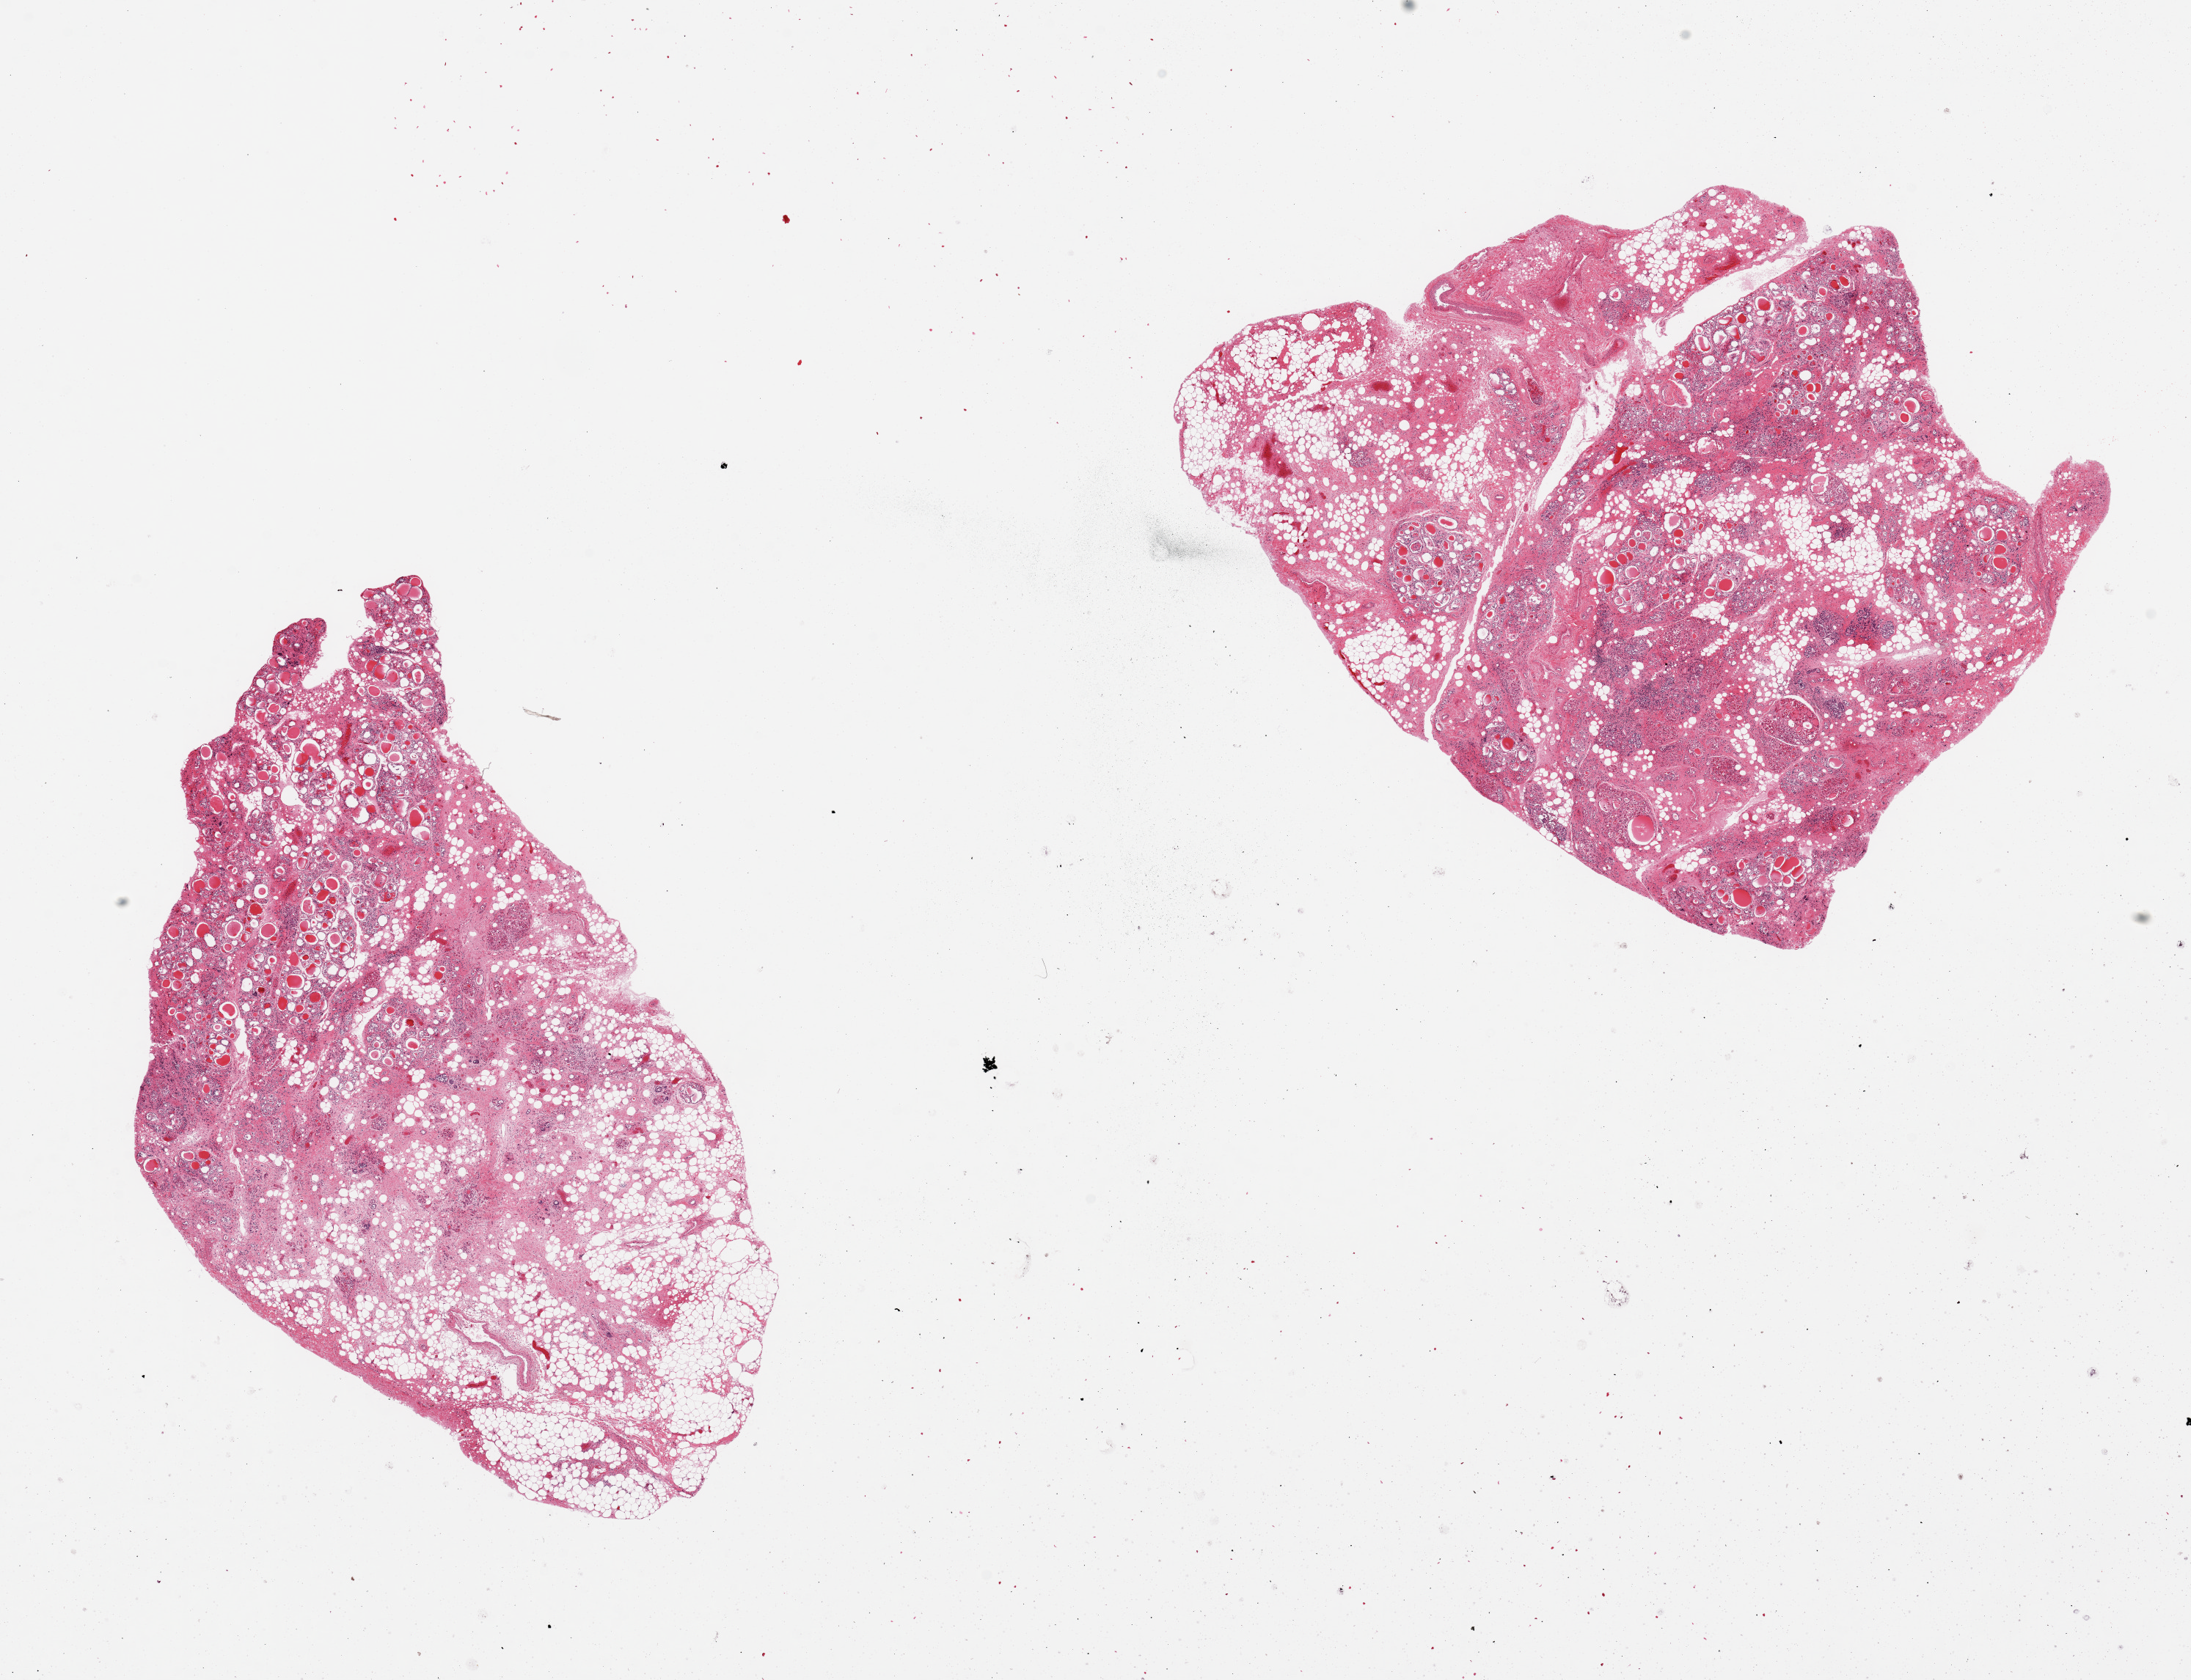
Hematoxylin and eosin (H&E) whole-slide image, a low-resolution overview of the entire scanned area, about 23.6 x 18.1 mm. PAXgene-fixed paraffin-embedded (PFPE) section. Target tissue: thyroid. Tissue donor sample. Donor sex: female.
* pathologist's review note for this sample: 2 pieces, 30-50% fat, fibrosis and atrophy, mild chronic inflammation, and some oncocytic change